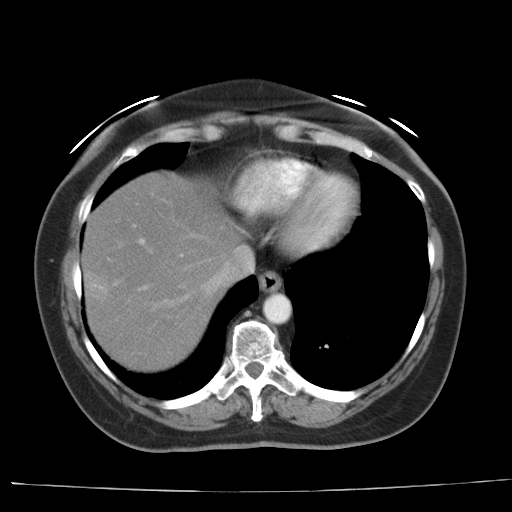
Contrast-enhanced abdominal CT, one axial slice. Slice 32 of 44 in the series (ordered by position). Reconstruction kernel AA-1. 140 kVp. Intravenous contrast given. Soft-tissue window (W 400 / L 40 HU). 512 × 512 image matrix, field of view 373 × 373 mm. Female patient. From the clinical record (not read from this slice): diagnosis: colorectal cancer liver metastases, imaged before liver resection; multiple liver metastases: yes; largest metastasis: 1.8 cm; chemotherapy before resection: yes.
Annotated regions visible in this slice (outlined manually by an expert reader):
- hepatic veins: bounding box <162,247,254,306> (left, top, right, bottom; pixels)
- liver: <82,172,245,372>
- planned liver remnant (the part of the liver to remain after resection): <114,172,246,273>
- portal vein (with intrahepatic branches): <113,239,244,289>